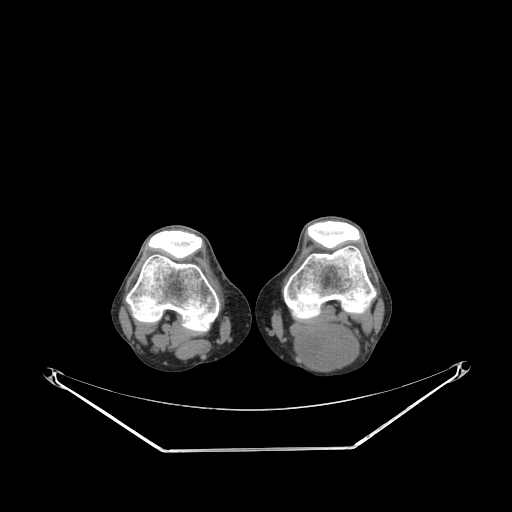
CT of an extremity soft-tissue mass (from a PET/CT study), one axial slice; position 181 of 267 along the scan axis; reconstruction kernel SOFT; 140 kVp; soft-tissue window (W 400 / L 40 HU); 3.75 mm slice thickness; 512 × 512 image matrix, field of view 500 × 500 mm. Male patient. Case-level facts recorded for this patient, not image findings: histological type: synovial sarcoma; site of the primary tumour: left poplietal fossa.
Annotated regions visible in this slice (expert contour drawn on MRI and transferred to this co-registered scan by the dataset authors):
- gross tumour volume (mass): bounding box [x1, y1, x2, y2] px = [292, 327, 359, 369]